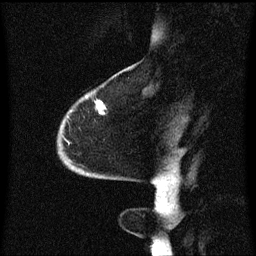
Breast MRI (dynamic contrast-enhanced), one sagittal slice. Dynamic contrast-enhanced series, image 2 of 3 at this slice position (ordered by acquisition). 1.5 T. TE 4.2 ms, TR 8.4 ms. 2 mm slice thickness. 256 × 256 image matrix, field of view 200 × 200 mm. Patient: female, 68 years. Case-level facts recorded for this patient, not image findings: setting: breast cancer imaged before/during neoadjuvant chemotherapy; receptor status: triple-negative.
Outlined on this slice (semi-automatically segmented with operator editing):
- analysis volume of interest (the breast-tissue region the enhancement analysis was run in; not a lesion): bounding box (x1, y1, x2, y2) in pixels: (59, 94, 108, 173)
- tumour enhancement mask (voxels above the 70 % enhancement threshold inside the analysis volume of interest): (97, 102, 106, 115)